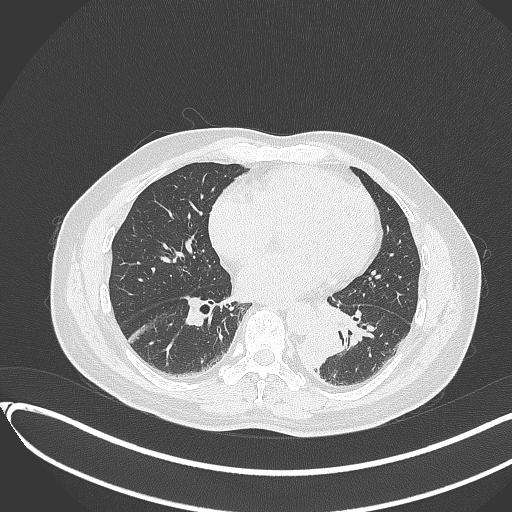
Chest CT, one axial slice. Position 137 of 417 along the scan axis. 120 kVp. Lung window (W 1500 / L -600 HU). 1 mm slice thickness. 512 × 512 image matrix. Male patient, age 54 years. Case-level facts recorded for this patient, not image findings: clinical TNM (as recorded): T3 N0 M0.
Structures marked on this image (rectangle marked by the reading radiologist):
- lung tumour (recorded histology: squamous cell carcinoma): bounding box (x1, y1, x2, y2) in pixels: (295, 327, 346, 372)